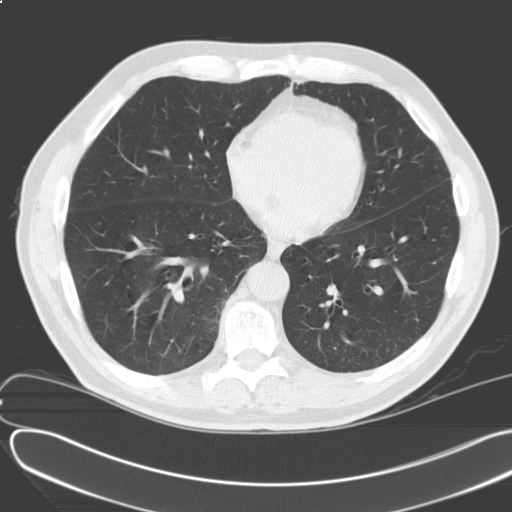
Axial slice from a low-dose chest CT screening exam; baseline annual screen; lung window (W 1500 / L -600 HU); slice 63 of 164 in the series. Male, age 69 years at enrolment. Former smoker at enrolment.
Lesion marked by an expert reader, bounding box <213,120,243,148> (left, top, right, bottom; pixels). The screening reader recorded 2 non-calcified nodules or masses ≥4 mm on this exam; which of them this box marks is not recorded.